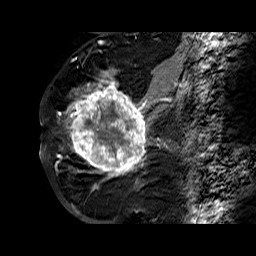
Breast MRI (dynamic contrast-enhanced), one sagittal slice. Slice 35 of 60 in the series (ordered by position). Dynamic contrast-enhanced series, time point 2 of 6 at this slice position (early post-contrast). 1.5 T. TE 6.3 ms, TR 32.4 ms. 4 mm slice thickness. 256 × 256 image matrix, field of view 200 × 200 mm. Female patient. From the clinical record (not read from this slice): setting: breast cancer imaged before/during neoadjuvant chemotherapy; receptor status: HR-positive, HER2-negative.
Annotated regions visible in this slice (semi-automatic segmentation, software-assisted and operator-edited):
- analysis volume of interest (the breast-tissue region the enhancement analysis was run in; not a lesion): bounding box (x1, y1, x2, y2) in pixels: (68, 72, 177, 181)
- tumour enhancement mask (voxels above the 100 % enhancement threshold inside the analysis volume of interest): (68, 72, 176, 180)